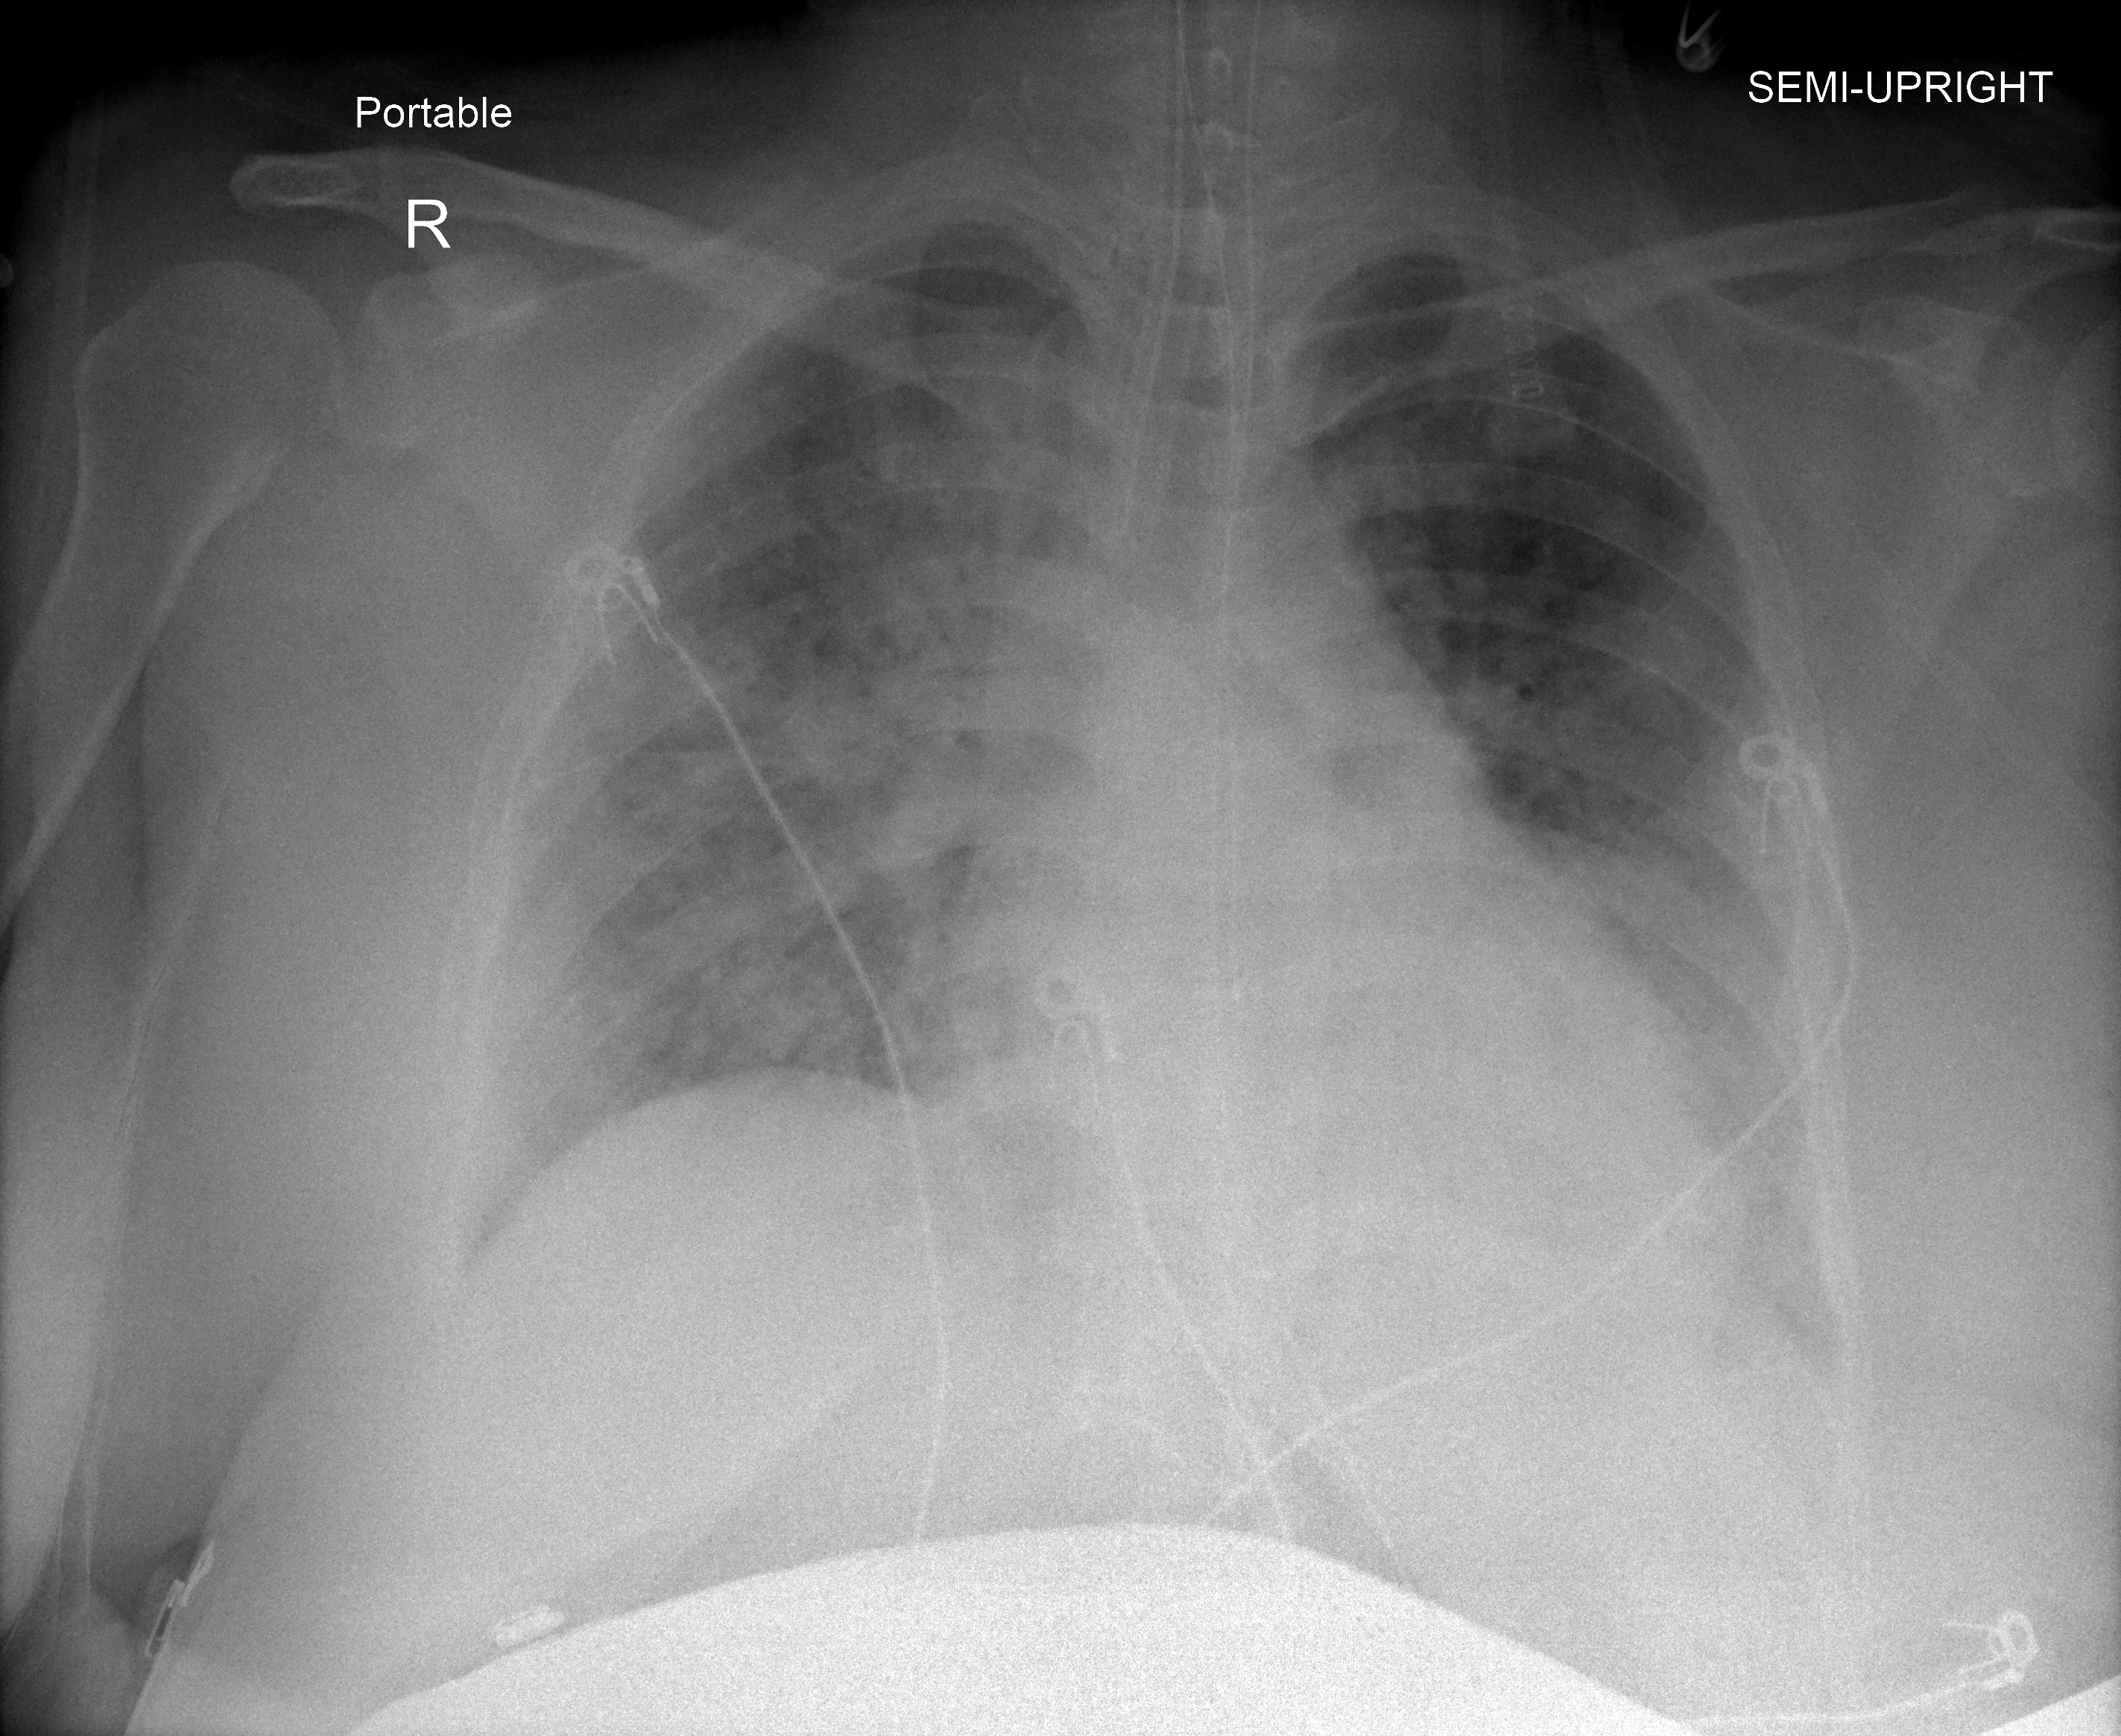
Portable chest radiograph, AP projection. Female patient, age 37 years; imaged 1 day after the COVID-19 diagnosis.
Radiologist's key findings for this exam: diffuse hazy lung opacities bilaterally most significant within the right perihilar region and bilateral lung bases.